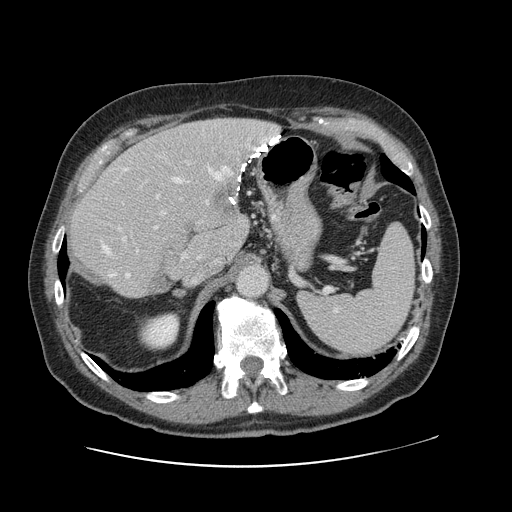
Contrast-enhanced abdominal CT, one axial slice; 120 kVp; intravenous contrast given; soft-tissue window (W 400 / L 40 HU); 512 × 512 image matrix, field of view 402 × 402 mm. Male patient, age 71 years. From the clinical record (not read from this slice): diagnosis: colorectal cancer liver metastases, imaged before liver resection; multiple liver metastases: no; largest metastasis: 3.3 cm; disease in both lobes: no.
Annotated regions visible in this slice (outlined manually by an expert reader):
- hepatic veins: box from (x=101, y=139) to (x=265, y=278) px
- liver: (x=70, y=119)–(x=276, y=297)
- planned liver remnant (the part of the liver to remain after resection): (x=69, y=150)–(x=237, y=297)
- portal vein (with intrahepatic branches): (x=122, y=161)–(x=190, y=258)
- liver metastasis: (x=211, y=183)–(x=237, y=216)